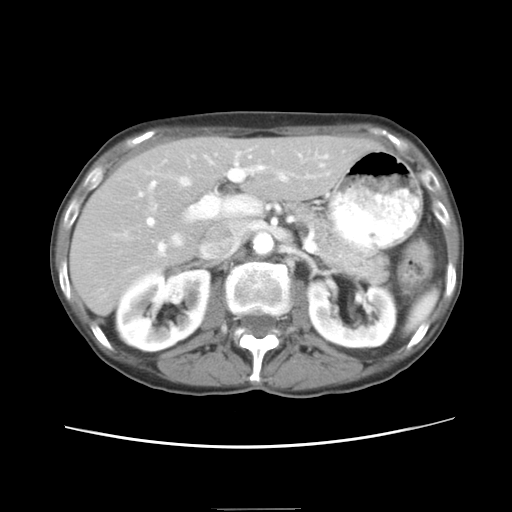
Contrast-enhanced abdominal CT, one axial slice; slice 13 of 26 in the series (ordered by position); reconstruction kernel STANDARD; 120 kVp; intravenous contrast given; soft-tissue window (W 400 / L 40 HU); 7.5 mm slice thickness; 512 × 512 image matrix, field of view 340 × 340 mm. Female patient, age 65 years. Case-level facts recorded for this patient, not image findings: diagnosis: colorectal cancer liver metastases, imaged before liver resection; multiple liver metastases: no; disease in both lobes: yes.
Outlined on this slice (expert manual segmentation):
- hepatic veins: bounding box <149,153,323,255> (left, top, right, bottom; pixels)
- liver: <72,138,373,312>
- planned liver remnant (the part of the liver to remain after resection): <72,138,372,312>
- portal vein (with intrahepatic branches): <138,152,282,255>